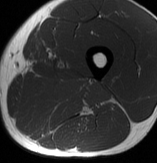
MRI of an extremity soft-tissue mass, one axial slice. Slice 31 of 70 in the series (ordered by position). MR volume resampled by the dataset authors to the PET/CT grid (not the native acquisition matrix). 157 × 163 image matrix, field of view 153 × 159 mm. Male patient. Case-level facts recorded for this patient, not image findings: histological type: extraskeletal osteosarcoma; grade: high; site of the primary tumour: left adductur.
Structures marked on this image (expert contour drawn on MRI and transferred to this co-registered scan by the dataset authors):
- gross tumour volume (mass): bounding box [x1, y1, x2, y2] px = [15, 72, 112, 136]